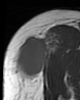
MRI of an extremity soft-tissue mass, one axial slice. Position 29 of 46 along the scan axis. MR volume resampled by the dataset authors to the PET/CT grid (not the native acquisition matrix). 80 × 100 image matrix, field of view 78 × 98 mm. Female patient. Case-level facts recorded for this patient, not image findings: histological type: synovial sarcoma; grade: intermediate; site of the primary tumour: right thigh.
Annotated regions visible in this slice (expert contour drawn on MRI and transferred to this co-registered scan by the dataset authors):
- gross tumour volume including surrounding oedema: bounding box [x1, y1, x2, y2] px = [14, 33, 59, 82]
- gross tumour volume (mass): [16, 35, 59, 82]